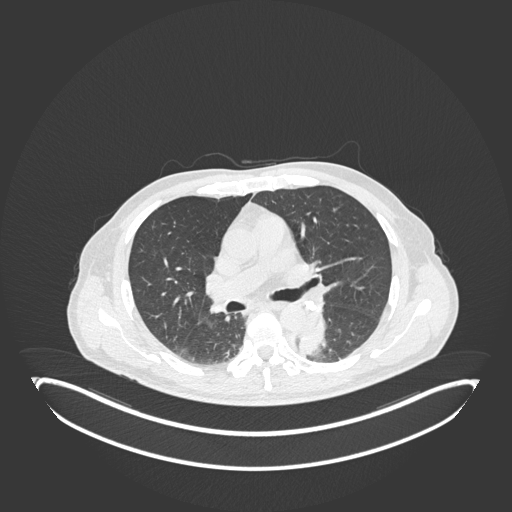
Chest CT, one axial slice; position 122 of 251 along the scan axis; reconstruction kernel B30f; 120 kVp; lung window (W 1500 / L -600 HU); 1 mm slice thickness; 512 × 512 image matrix. Patient: male, 72 years. Case-level facts recorded for this patient, not image findings: clinical TNM (as recorded): T2b N0 M1.
Annotated regions visible in this slice (bounding box drawn by a radiologist):
- lung tumour (recorded histology: adenocarcinoma): bounding box (x1, y1, x2, y2) in pixels: (299, 308, 330, 359)